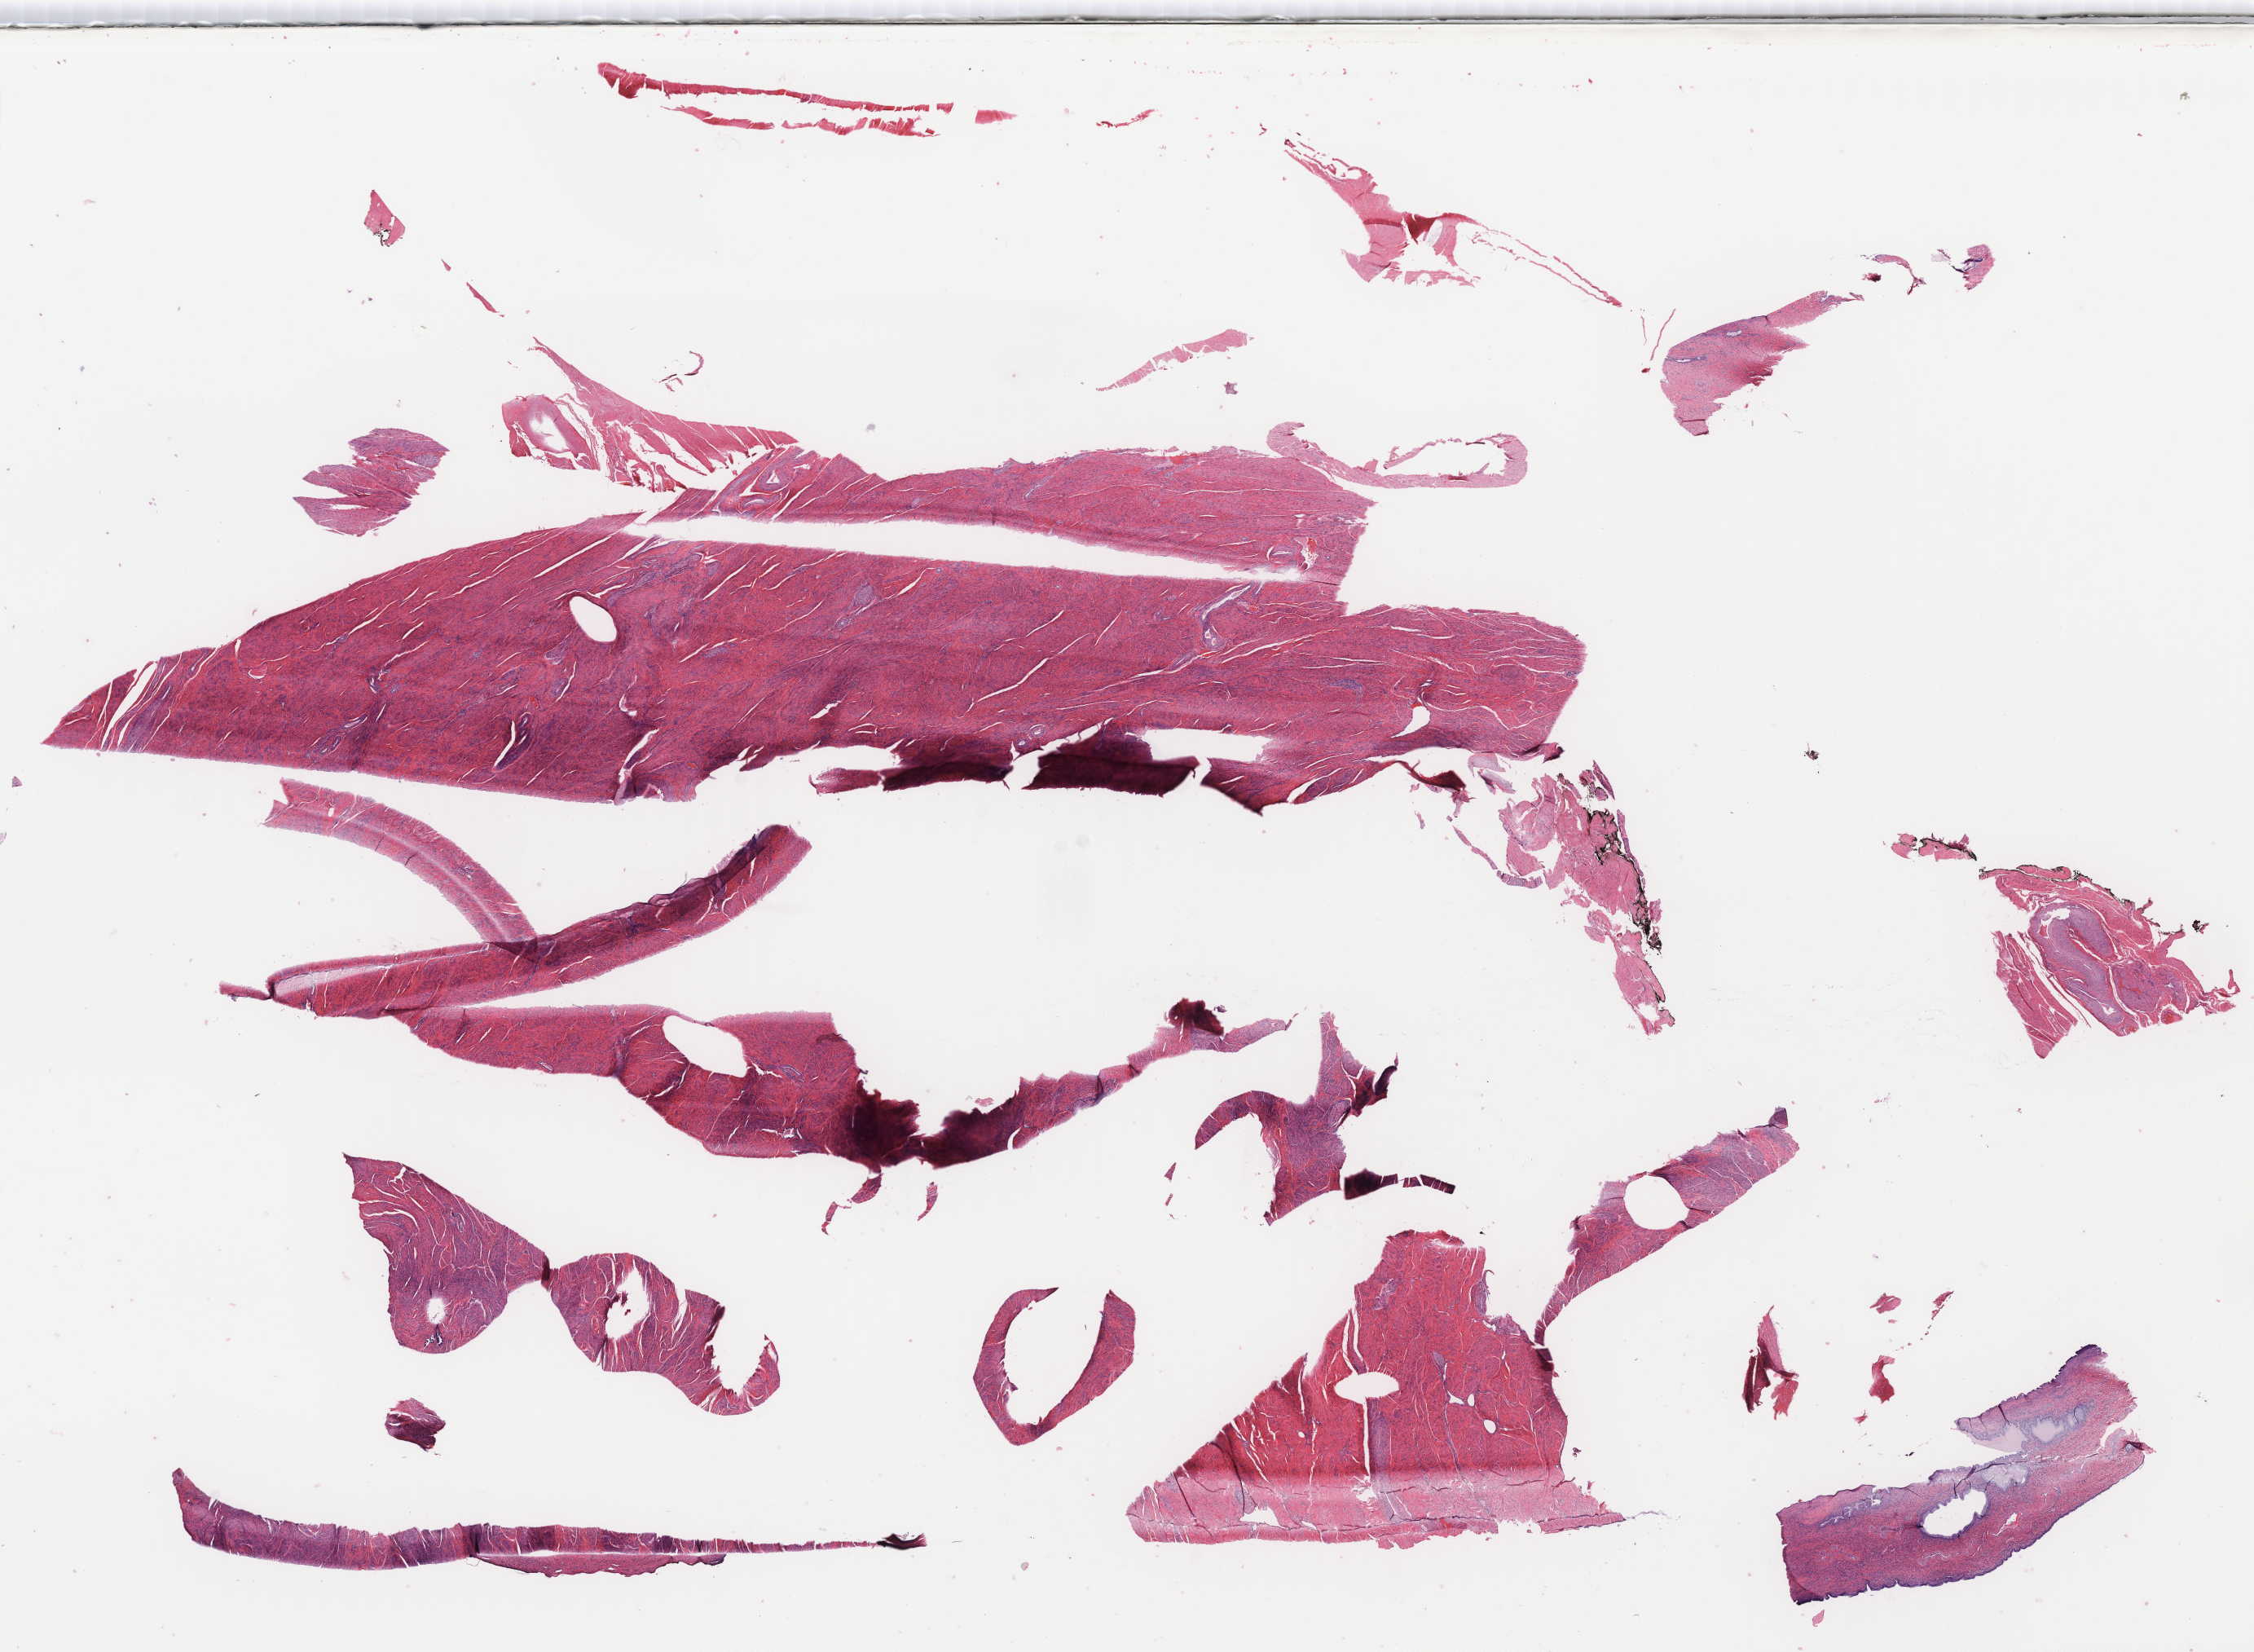
Whole-slide image, hematoxylin and eosin (H&E) stain — whole scanned area (about 21.9 x 16.0 mm) shown as a low-resolution overview. Frozen section (tissue freezing medium). Specimen: non-tumor (normal tissue) sample from a patient with carcinosarcoma, NOS. Site: endometrium. Female patient. Pathologist review of this section (percent, as recorded): tumor cells 0%, tumor nuclei 0%, stromal cells 80%, necrosis 0%, normal cells 20%. Infiltration values recorded for this section: lymphocyte infiltration 5%, monocyte infiltration 3%, neutrophil infiltration 7%.
• this section: non-tumor tissue sample; the patient's diagnosis is given above
• section: top of the tissue portion